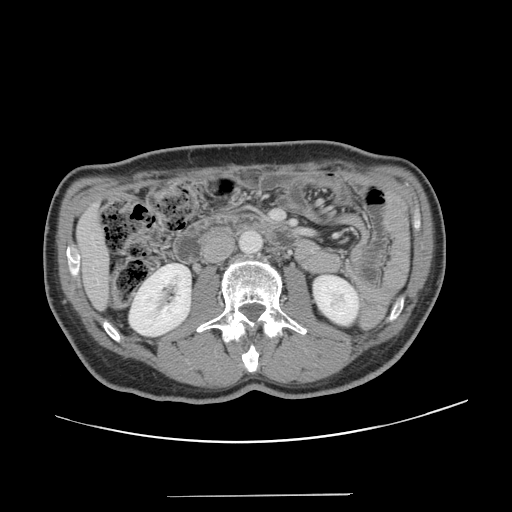
Contrast-enhanced abdominal CT, one axial slice. Position 48 of 131 along the scan axis. 120 kVp. Intravenous contrast given. Soft-tissue window (W 400 / L 40 HU). 2.5 mm slice thickness. 512 × 512 image matrix, field of view 403 × 403 mm. Male patient, age 60 years. From the clinical record (not read from this slice): diagnosis: colorectal cancer liver metastases, imaged before liver resection.
Outlined on this slice (expert manual segmentation):
- liver: bounding box [x1, y1, x2, y2] px = [79, 210, 108, 308]
- planned liver remnant (the part of the liver to remain after resection): [79, 210, 108, 307]